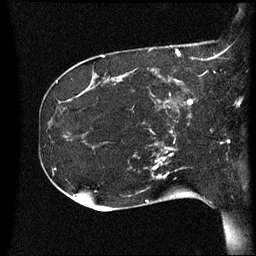
Breast MRI (dynamic contrast-enhanced), one sagittal slice. Position 18 of 60 along the scan axis. Dynamic contrast-enhanced series, image 2 of 3 at this slice position (ordered by acquisition). 1.5 T. TE 4.2 ms, TR 8.4 ms. 2.2 mm slice thickness. 256 × 256 image matrix. Female patient, age 41 years. From the clinical record (not read from this slice): setting: breast cancer imaged before/during neoadjuvant chemotherapy; receptor status: HER2-positive.
Structures marked on this image (semi-automatically segmented with operator editing):
- analysis volume of interest (the breast-tissue region the enhancement analysis was run in; not a lesion): box from (x=122, y=80) to (x=194, y=125) px
- tumour enhancement mask (voxels above the 70 % enhancement threshold inside the analysis volume of interest): (x=165, y=100)–(x=194, y=105)